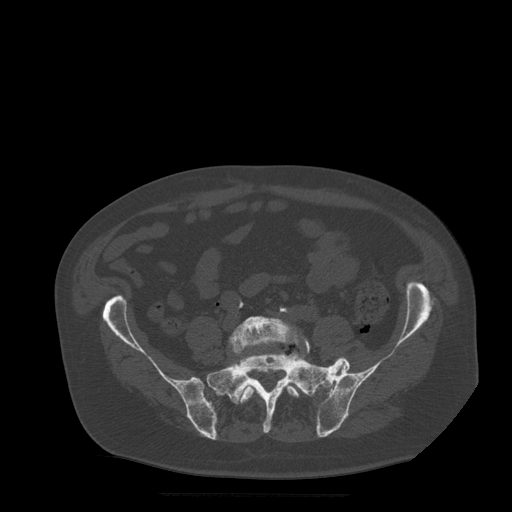
CT including the spine, one axial slice. Position 74 of 522 along the scan axis. Bone window (W 1800 / L 400 HU). 512 × 512 image matrix. Patient age 72 years. Case-level facts recorded for this patient, not image findings: primary cancer: prostate.
Annotated regions visible in this slice (semi-automatically segmented with operator editing):
- L5 vertebra: bounding box <229,316,311,403> (left, top, right, bottom; pixels)